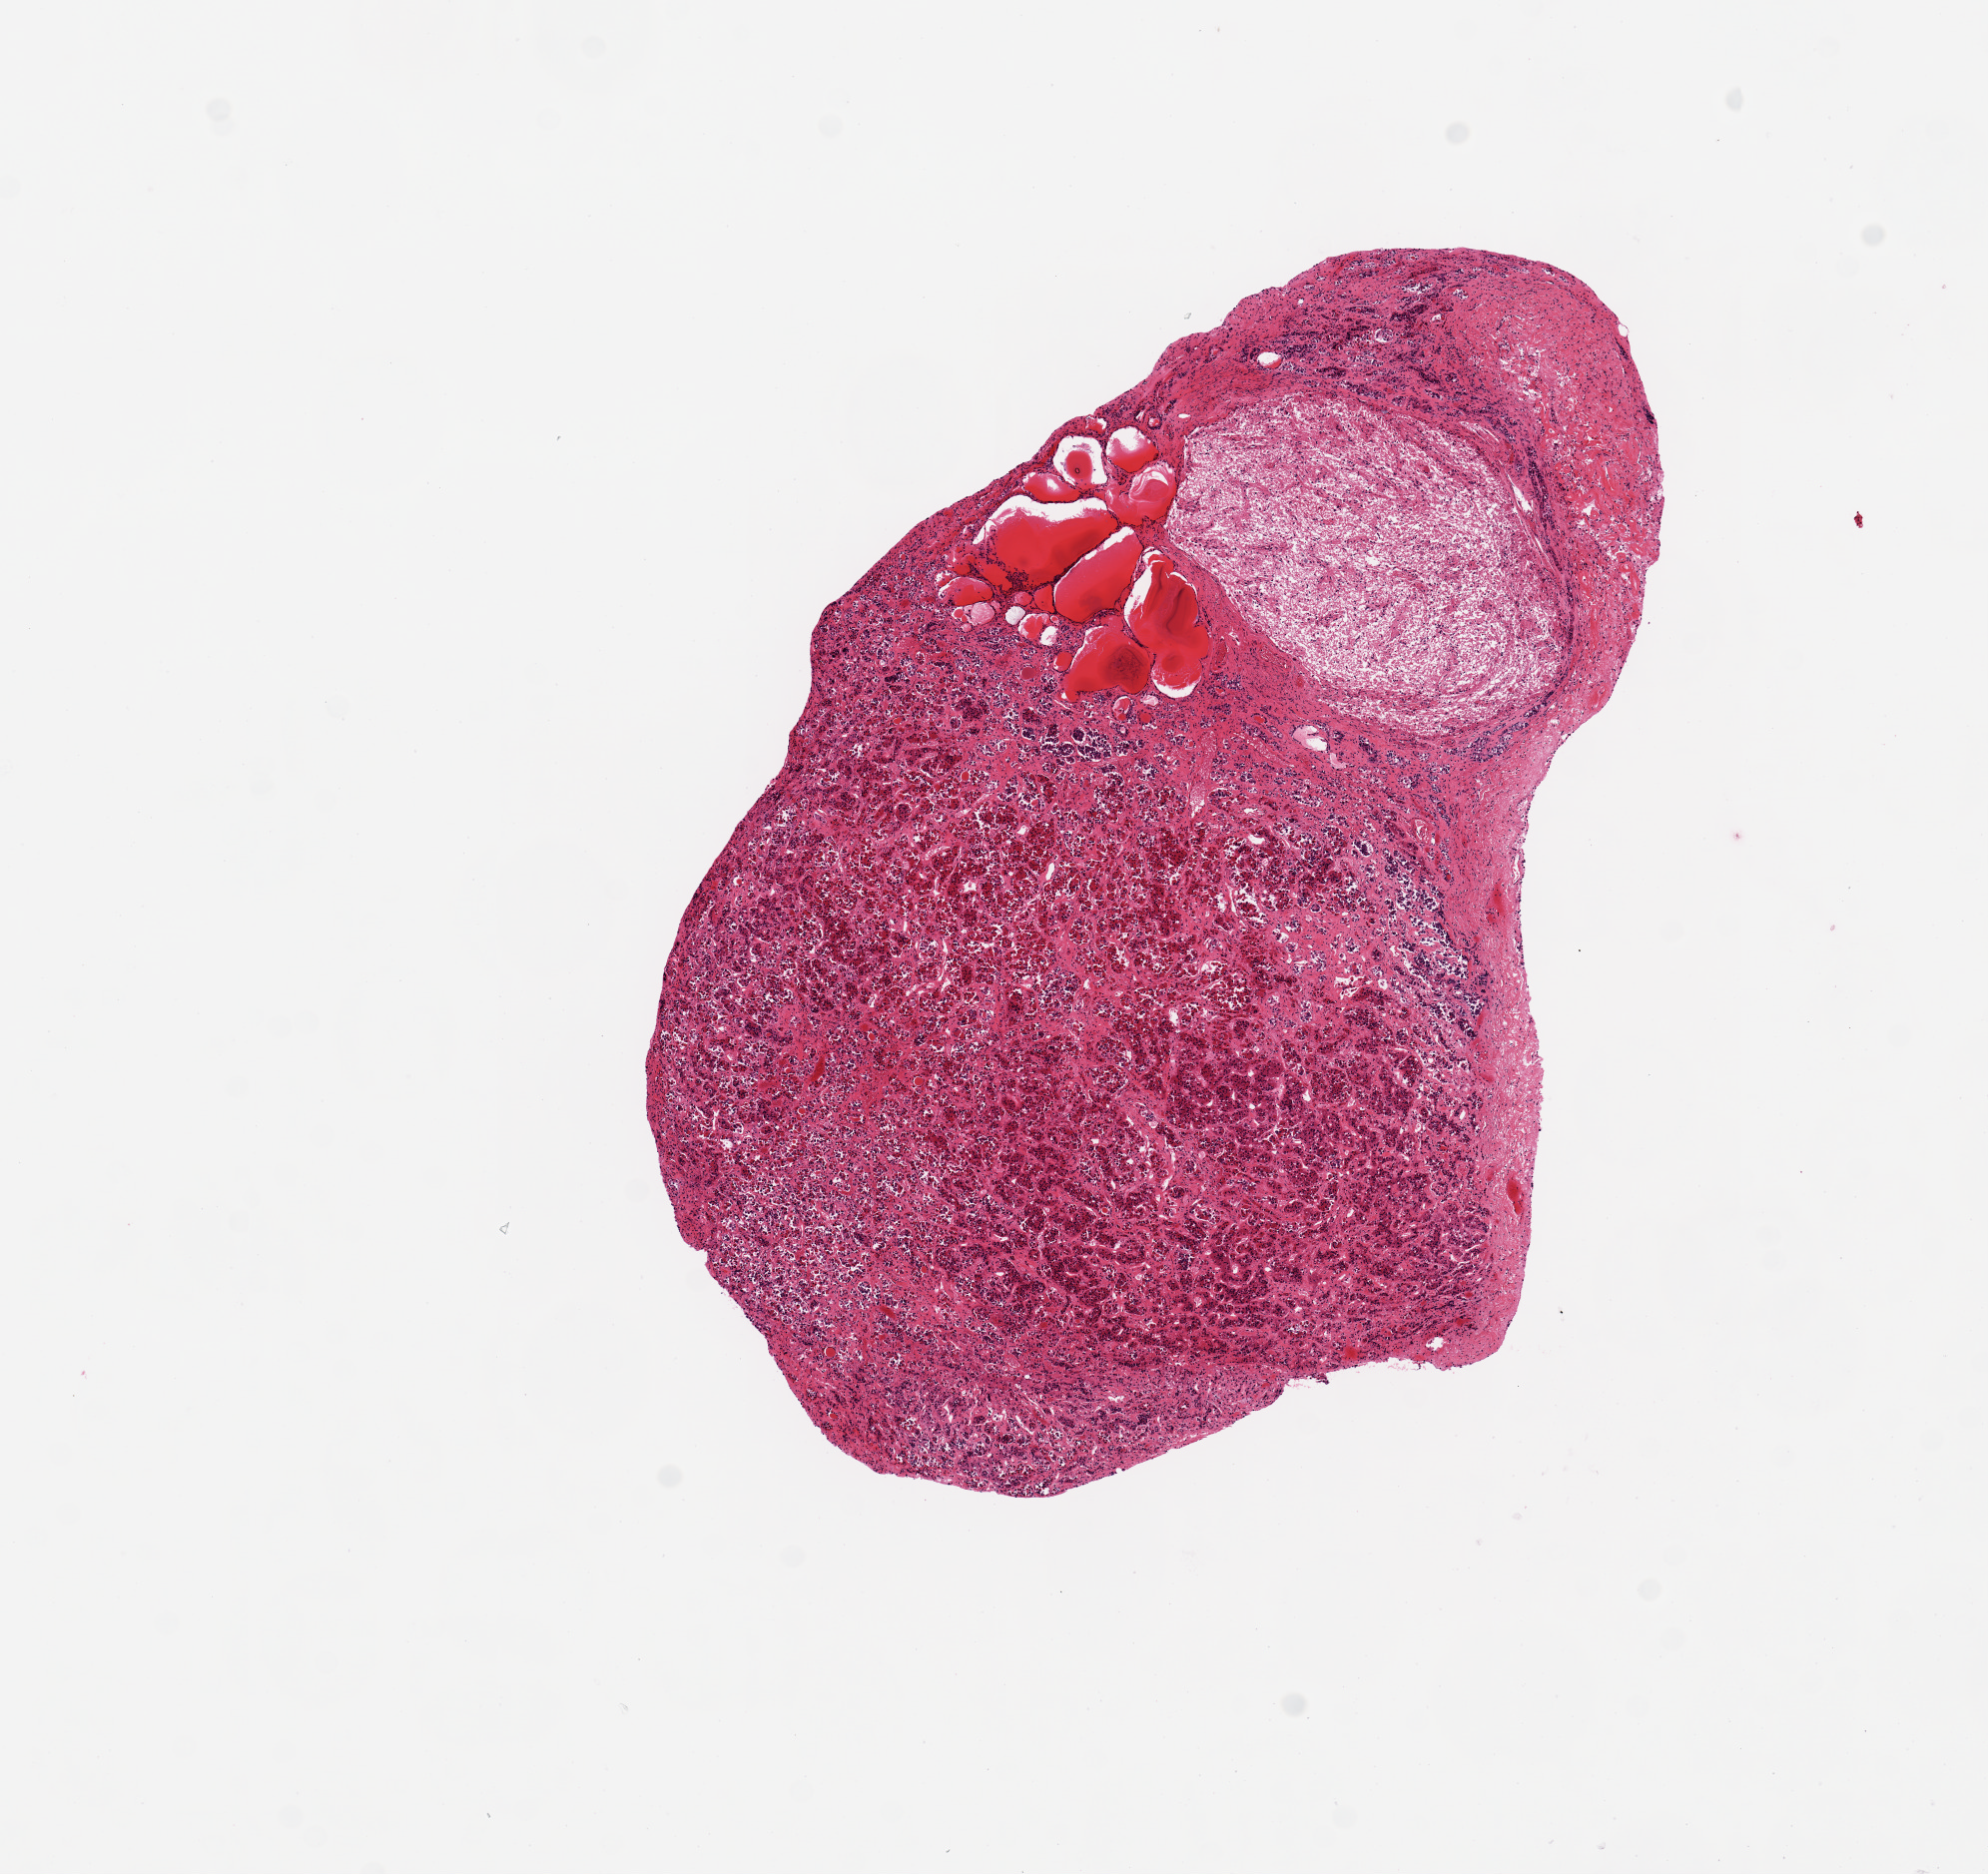
Whole-slide image, H&E stain, a low-resolution overview of the entire scanned area, about 7.9 x 7.4 mm (acquisition: 20x scan), PAXgene-fixed paraffin-embedded (PFPE) section, section of pituitary (target tissue), donor tissue sample. Male donor.
Review note (as recorded): Anterior and posterior present.